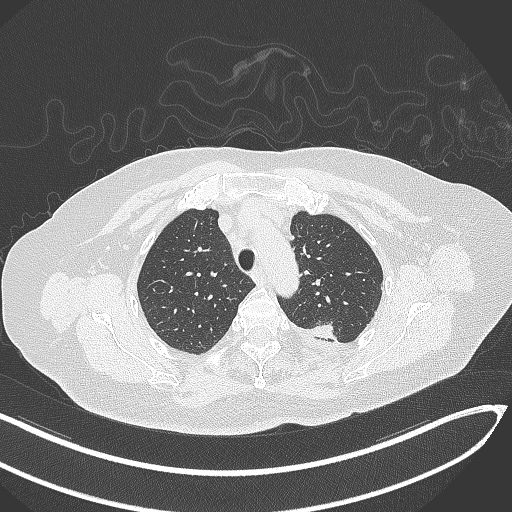
Chest CT, one axial slice. Slice 252 of 270 in the series (ordered by position). Reconstruction kernel B70f. 120 kVp. Lung window (W 1500 / L -600 HU). 1 mm slice thickness. 512 × 512 image matrix, field of view 400 × 400 mm. Female patient, age 76 years. Case-level facts recorded for this patient, not image findings: clinical TNM (as recorded): T1c N0 M0.
Structures marked on this image (bounding box drawn by a radiologist):
- lung tumour (recorded histology: adenocarcinoma): bounding box <311,322,337,342> (left, top, right, bottom; pixels)